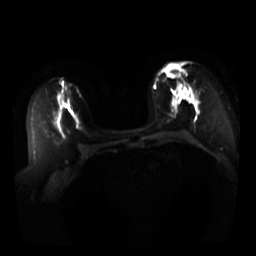
Breast MRI, one axial slice; position 19 of 44 along the scan axis; diffusion-weighted series; image 2 of 4 stored at this slice position (different b-values; order by instance number); 3 T; 5 mm slice thickness; 256 × 256 image matrix, field of view 340 × 340 mm. Female patient.
Annotated regions visible in this slice (outlined manually by an expert reader):
- tumour on diffusion-weighted imaging: bounding box <165,65,187,100> (left, top, right, bottom; pixels)